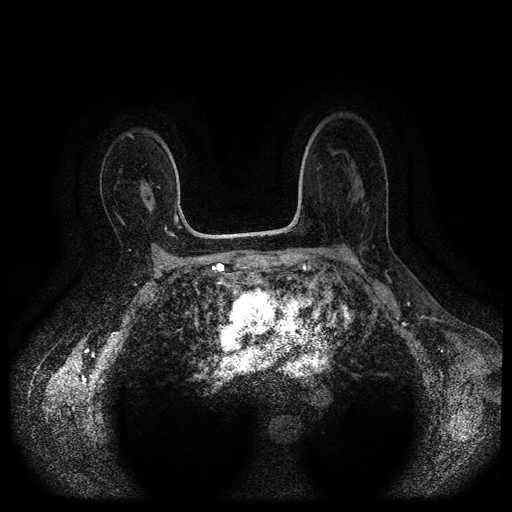
Breast MRI (dynamic contrast-enhanced, multi-phase), one axial slice. Position 60 of 112 along the scan axis. Dynamic contrast-enhanced series, time point 2 of 5 at this slice position (early post-contrast). 1.5 T. TE 2.6 ms, TR 5.4 ms. 2 mm slice thickness. 512 × 512 image matrix, field of view 340 × 340 mm. Female patient, age 53 years.
Outlined on this slice (semi-automatic segmentation, software-assisted and operator-edited):
- breast lesion (labelled 'tumour' in the annotation; benign lesions carry a separate 'benign' label): box from (x=134, y=182) to (x=155, y=213) px